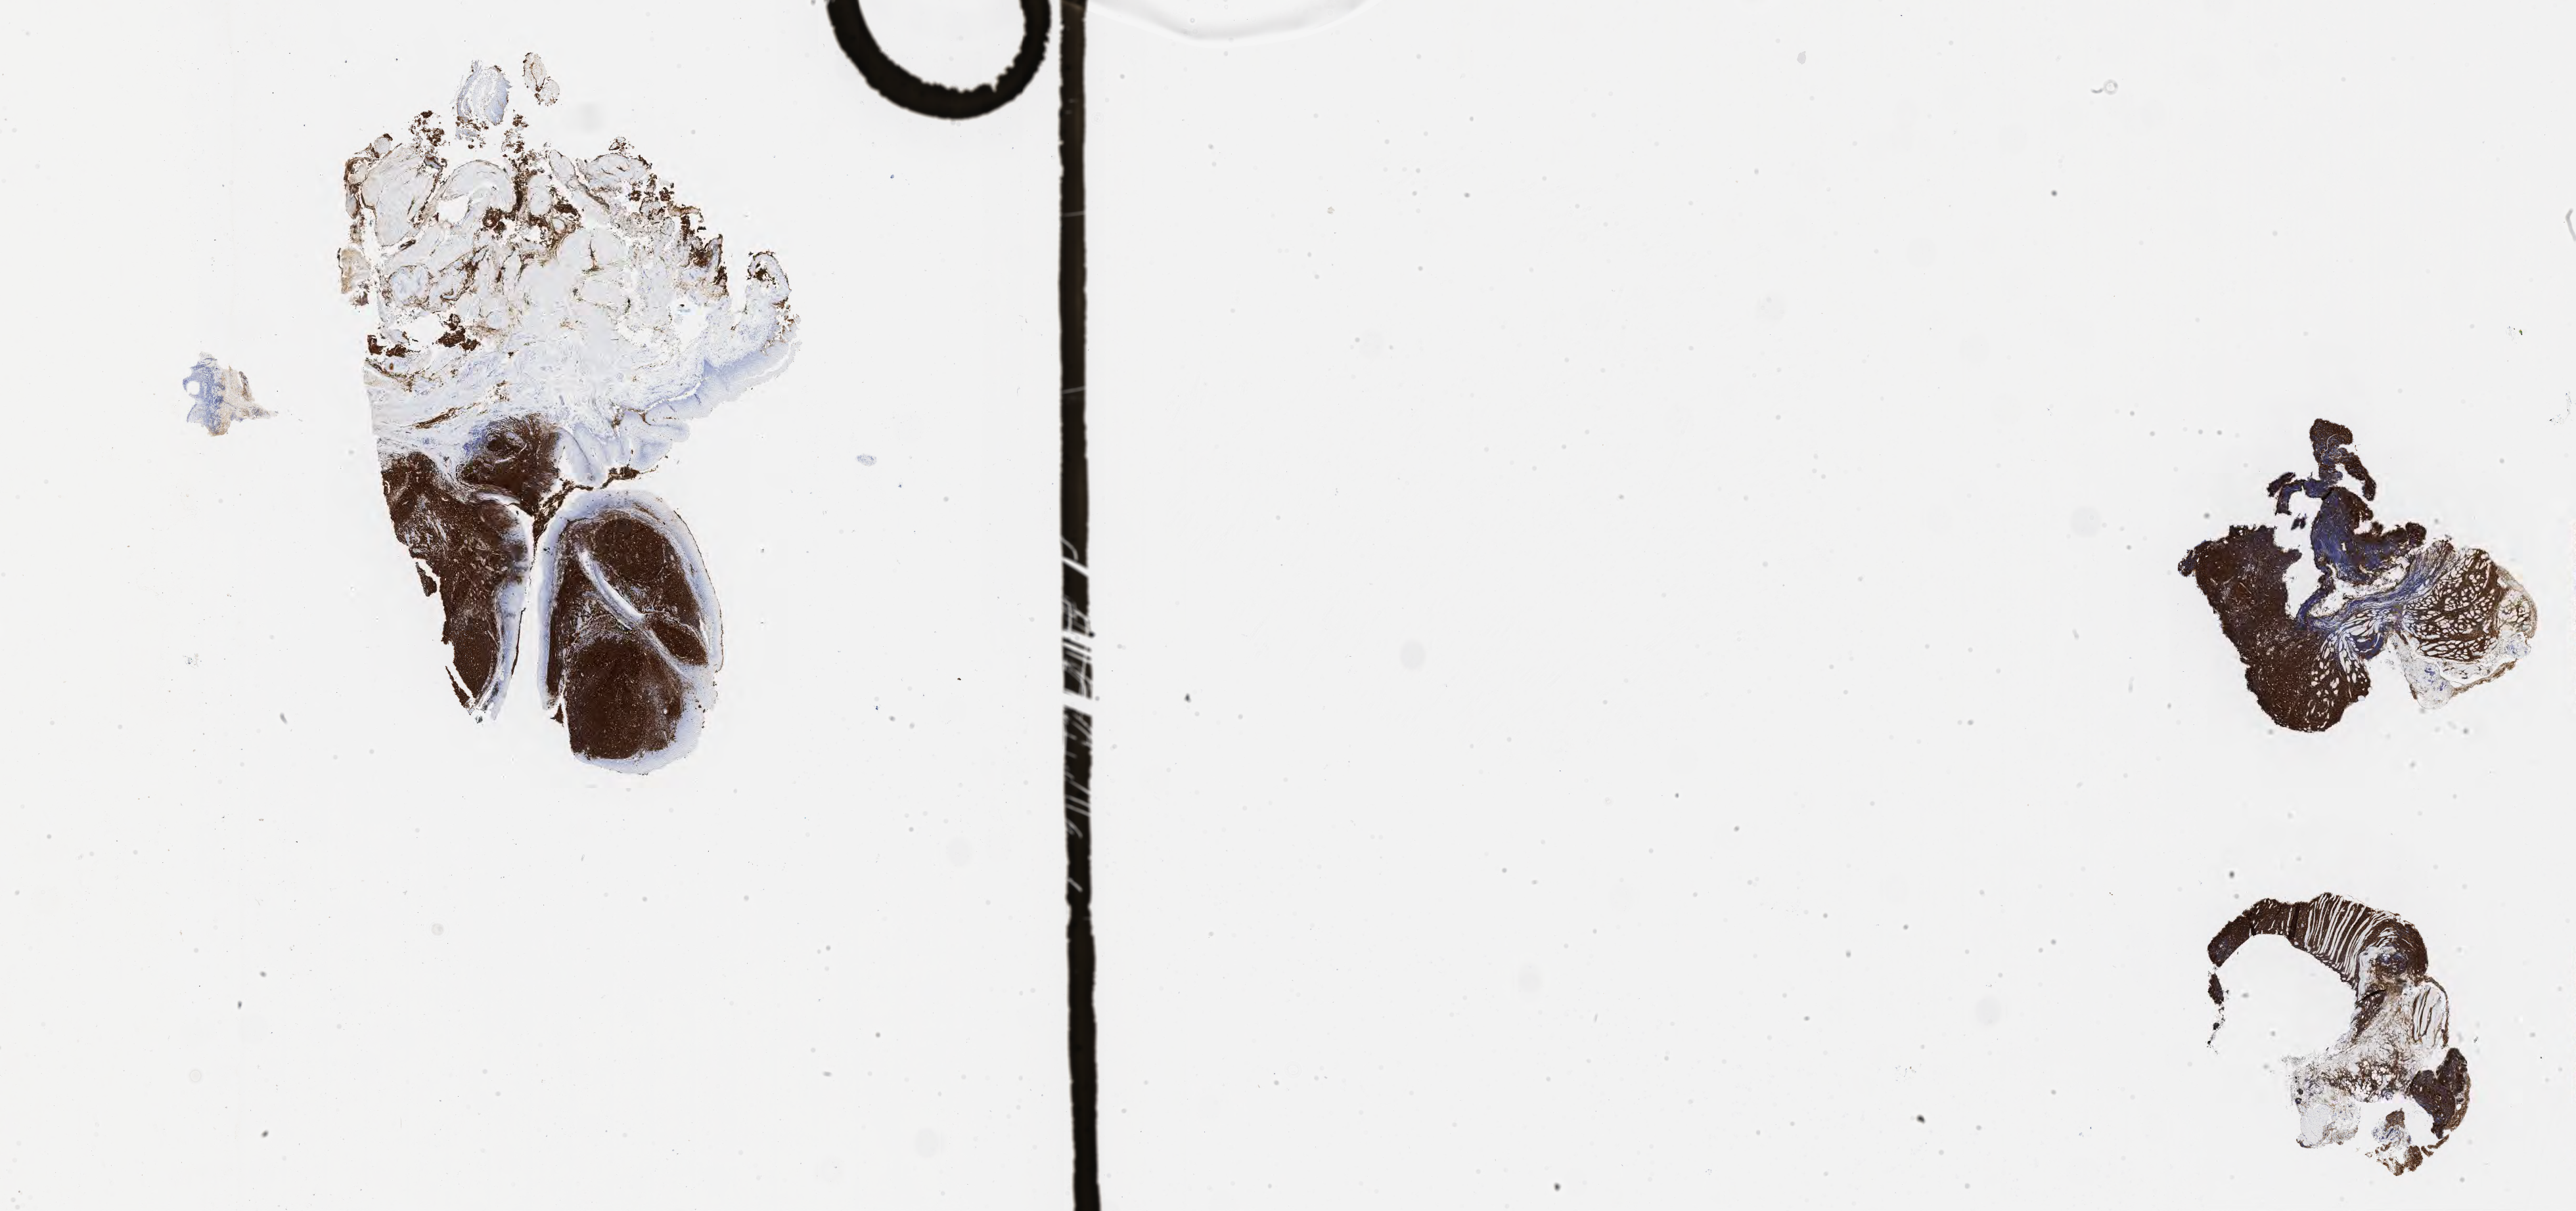
IHC for CD20, whole-slide image, whole scanned area (about 31.7 x 14.9 mm) shown as a low-resolution overview. Tumor tissue. Anatomic site: lymph node of head and neck. Male patient, 73 years old.
- diagnosis: Burkitt lymphoma, NOS